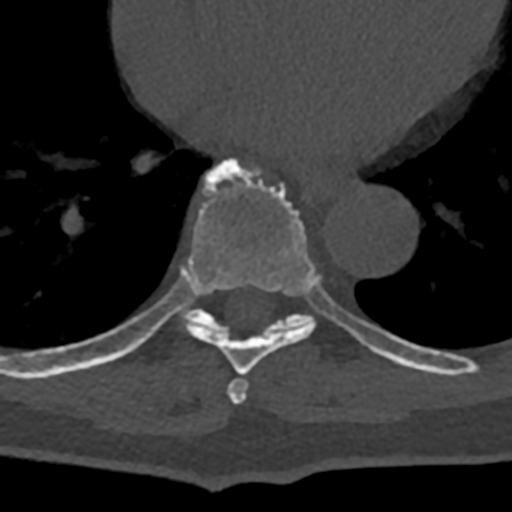
CT including the spine, one axial slice. Position 694 of 797 along the scan axis. Reconstruction kernel Br40s/3. 120 kVp. Bone window (W 1800 / L 400 HU). 512 × 512 image matrix, field of view 160 × 160 mm. Patient: male, 74 years. Case-level facts recorded for this patient, not image findings: primary cancer: renal.
Structures marked on this image (semi-automatically segmented with operator editing):
- T7 vertebra: bounding box (x1, y1, x2, y2) in pixels: (227, 378, 247, 404)
- T8 vertebra: (70, 158, 395, 375)
- T9 vertebra: (161, 270, 432, 373)